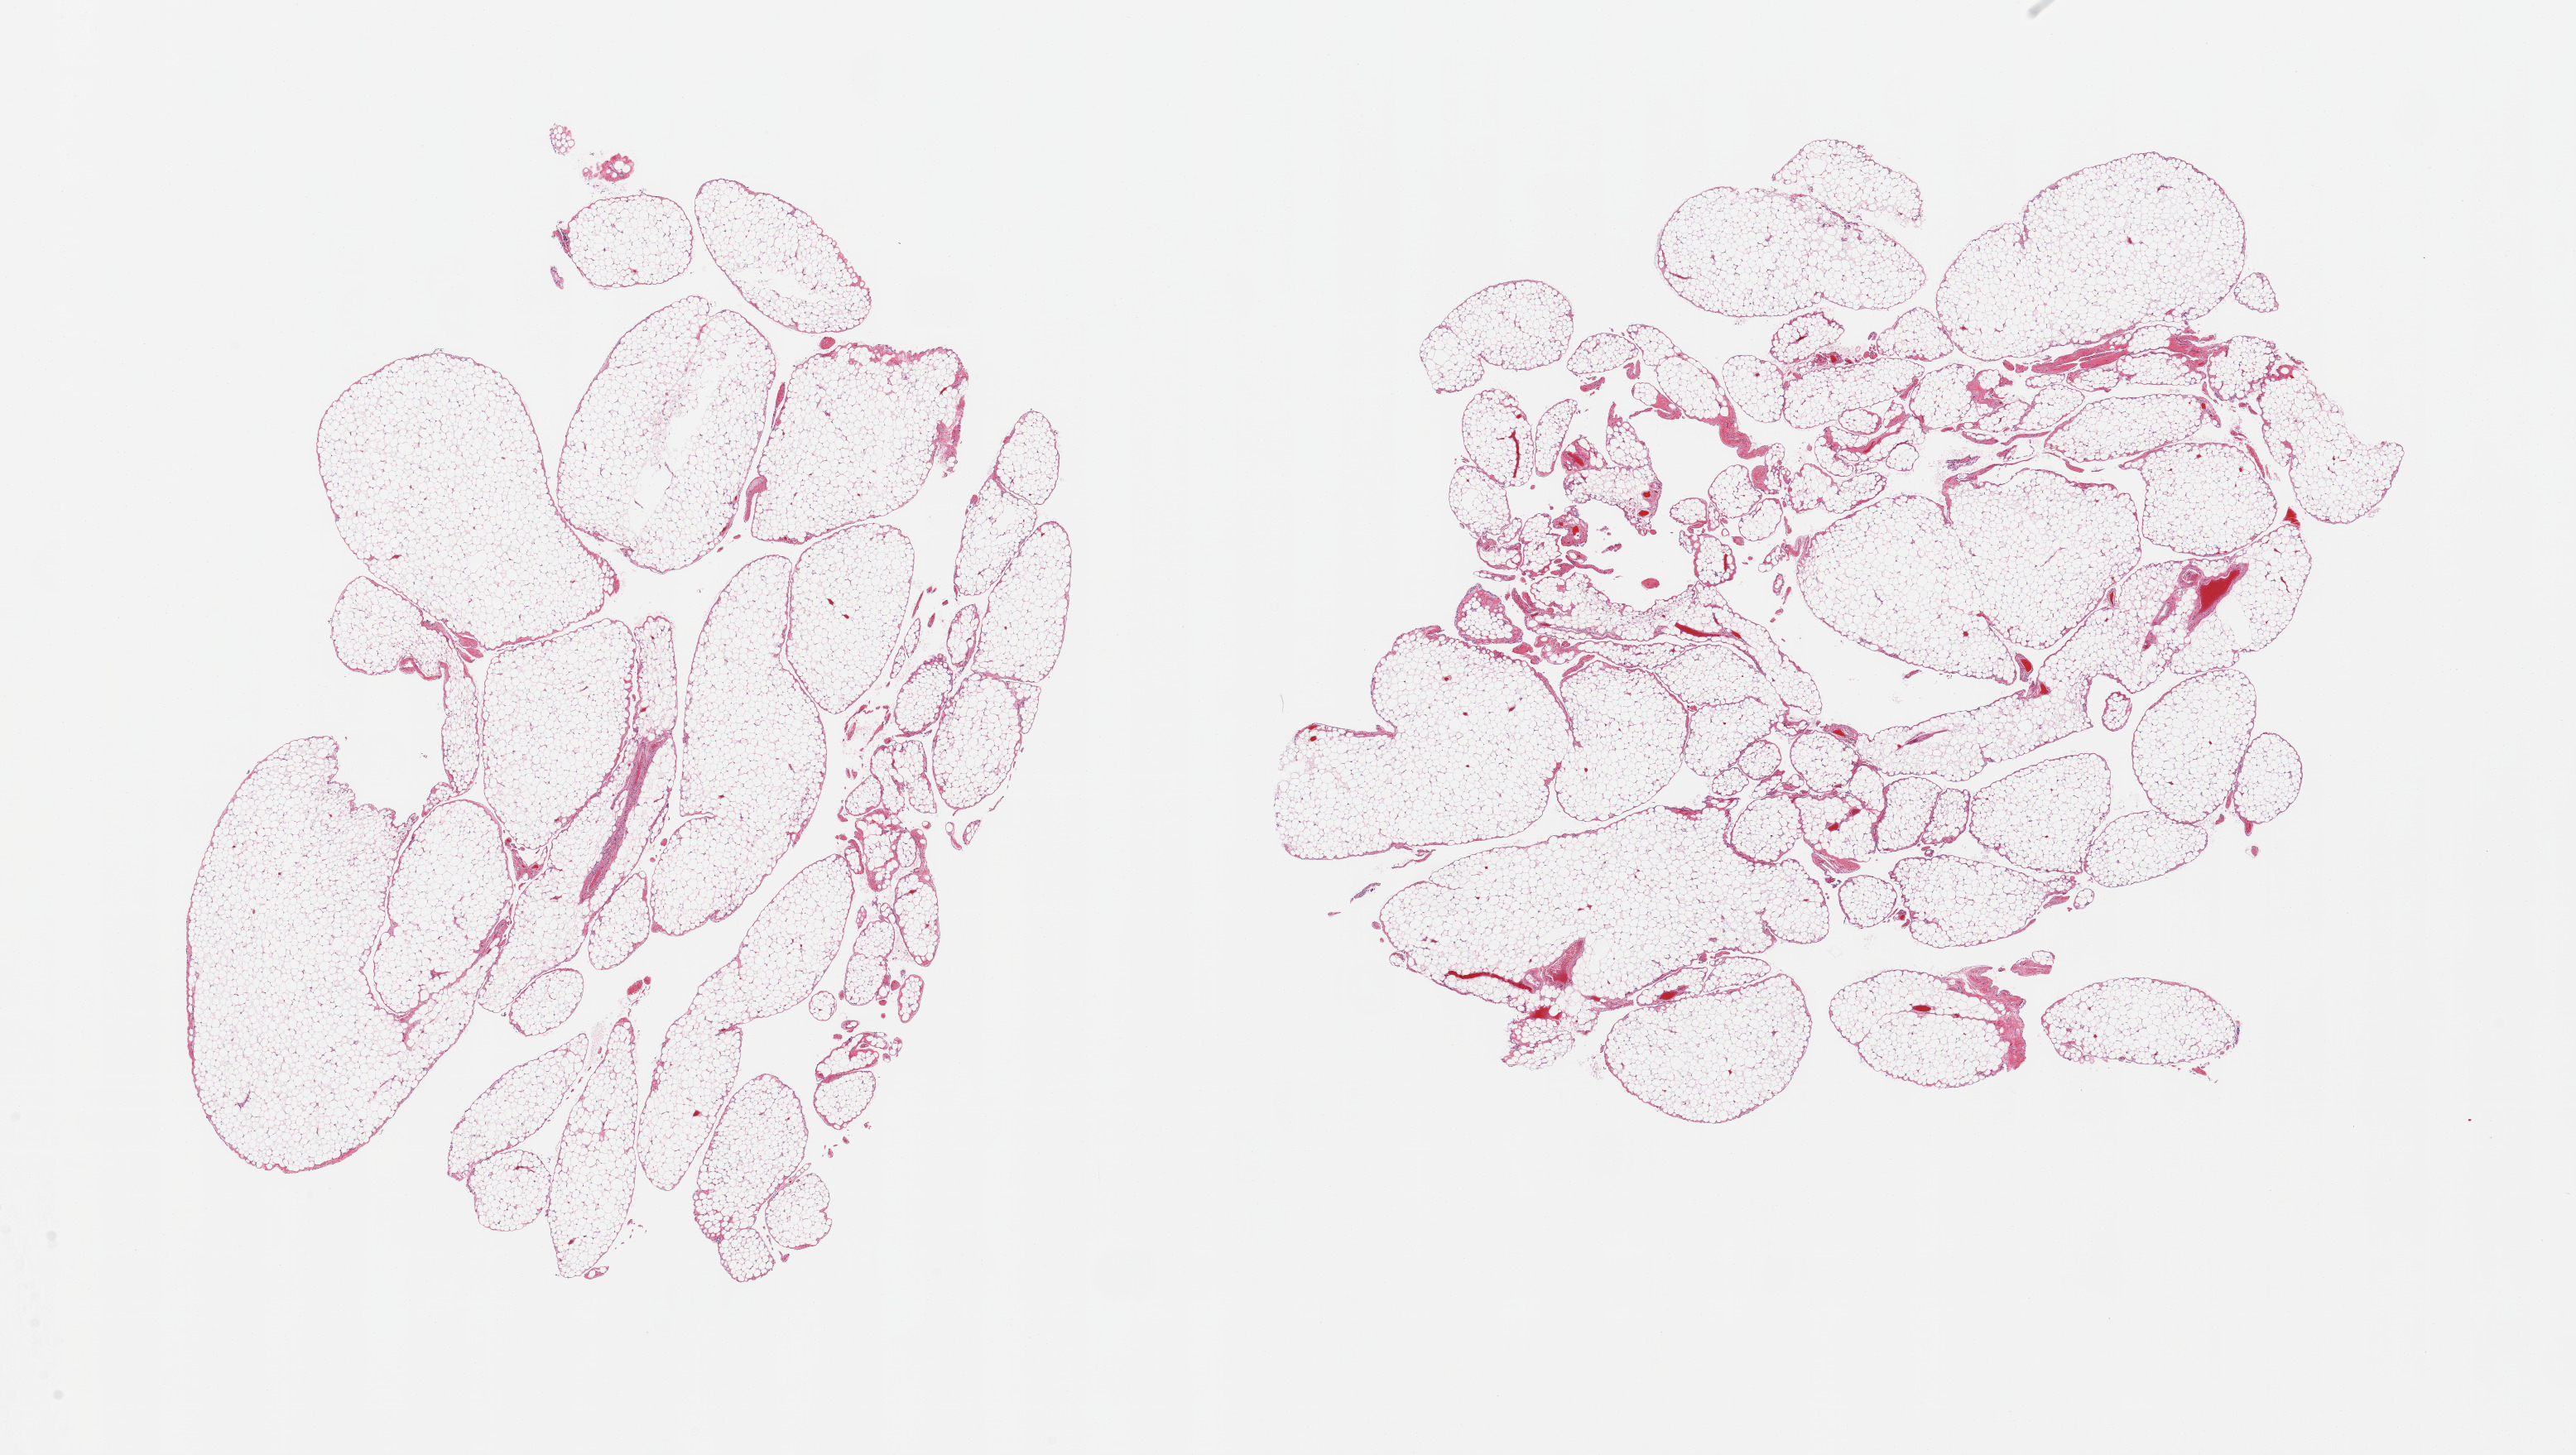
Whole-slide image, haematoxylin and eosin stain — low-resolution overview of the scanned area, about 24.6 x 13.9 mm; PAXgene-fixed paraffin-embedded (PFPE) section; target tissue: omentum; tissue donor sample. Donor sex: male.
* pathologist's review note for this sample: 2 pieces, trace fascia/vascular elements